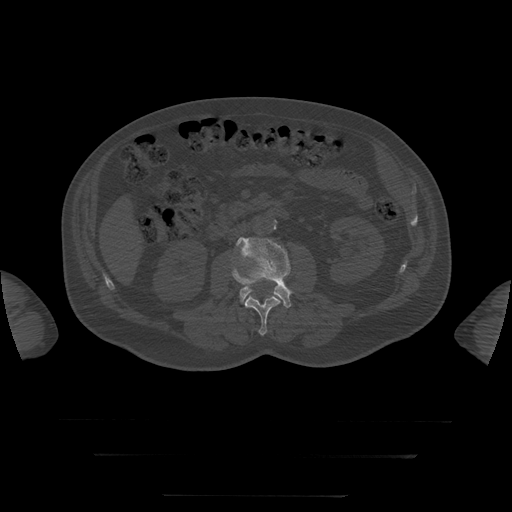
CT including the spine, one axial slice; position 11 of 397 along the scan axis; reconstruction kernel STANDARD; 120 kVp; bone window (W 1800 / L 400 HU); 1.25 mm slice thickness; 512 × 512 image matrix, field of view 510 × 510 mm. Patient age 73 years. Case-level facts recorded for this patient, not image findings: primary cancer: prostate.
Structures marked on this image (semi-automatically segmented with operator editing):
- L3 vertebra: bounding box <236,237,292,308> (left, top, right, bottom; pixels)